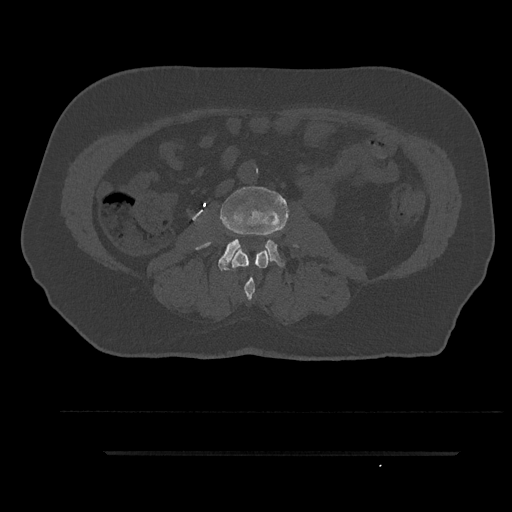
CT including the spine, one axial slice. Slice 70 of 797 in the series (ordered by position). Reconstruction kernel Br40s/3. Bone window (W 1800 / L 400 HU). 0.5 mm slice thickness. 512 × 512 image matrix. Male patient, age 63 years. Case-level facts recorded for this patient, not image findings: primary cancer: renal; vertebrae with lytic lesions (as recorded): T8.
Outlined on this slice (semi-automatically segmented with operator editing):
- L2 vertebra: bounding box (x1, y1, x2, y2) in pixels: (232, 250, 268, 301)
- L3 vertebra: (201, 185, 296, 270)